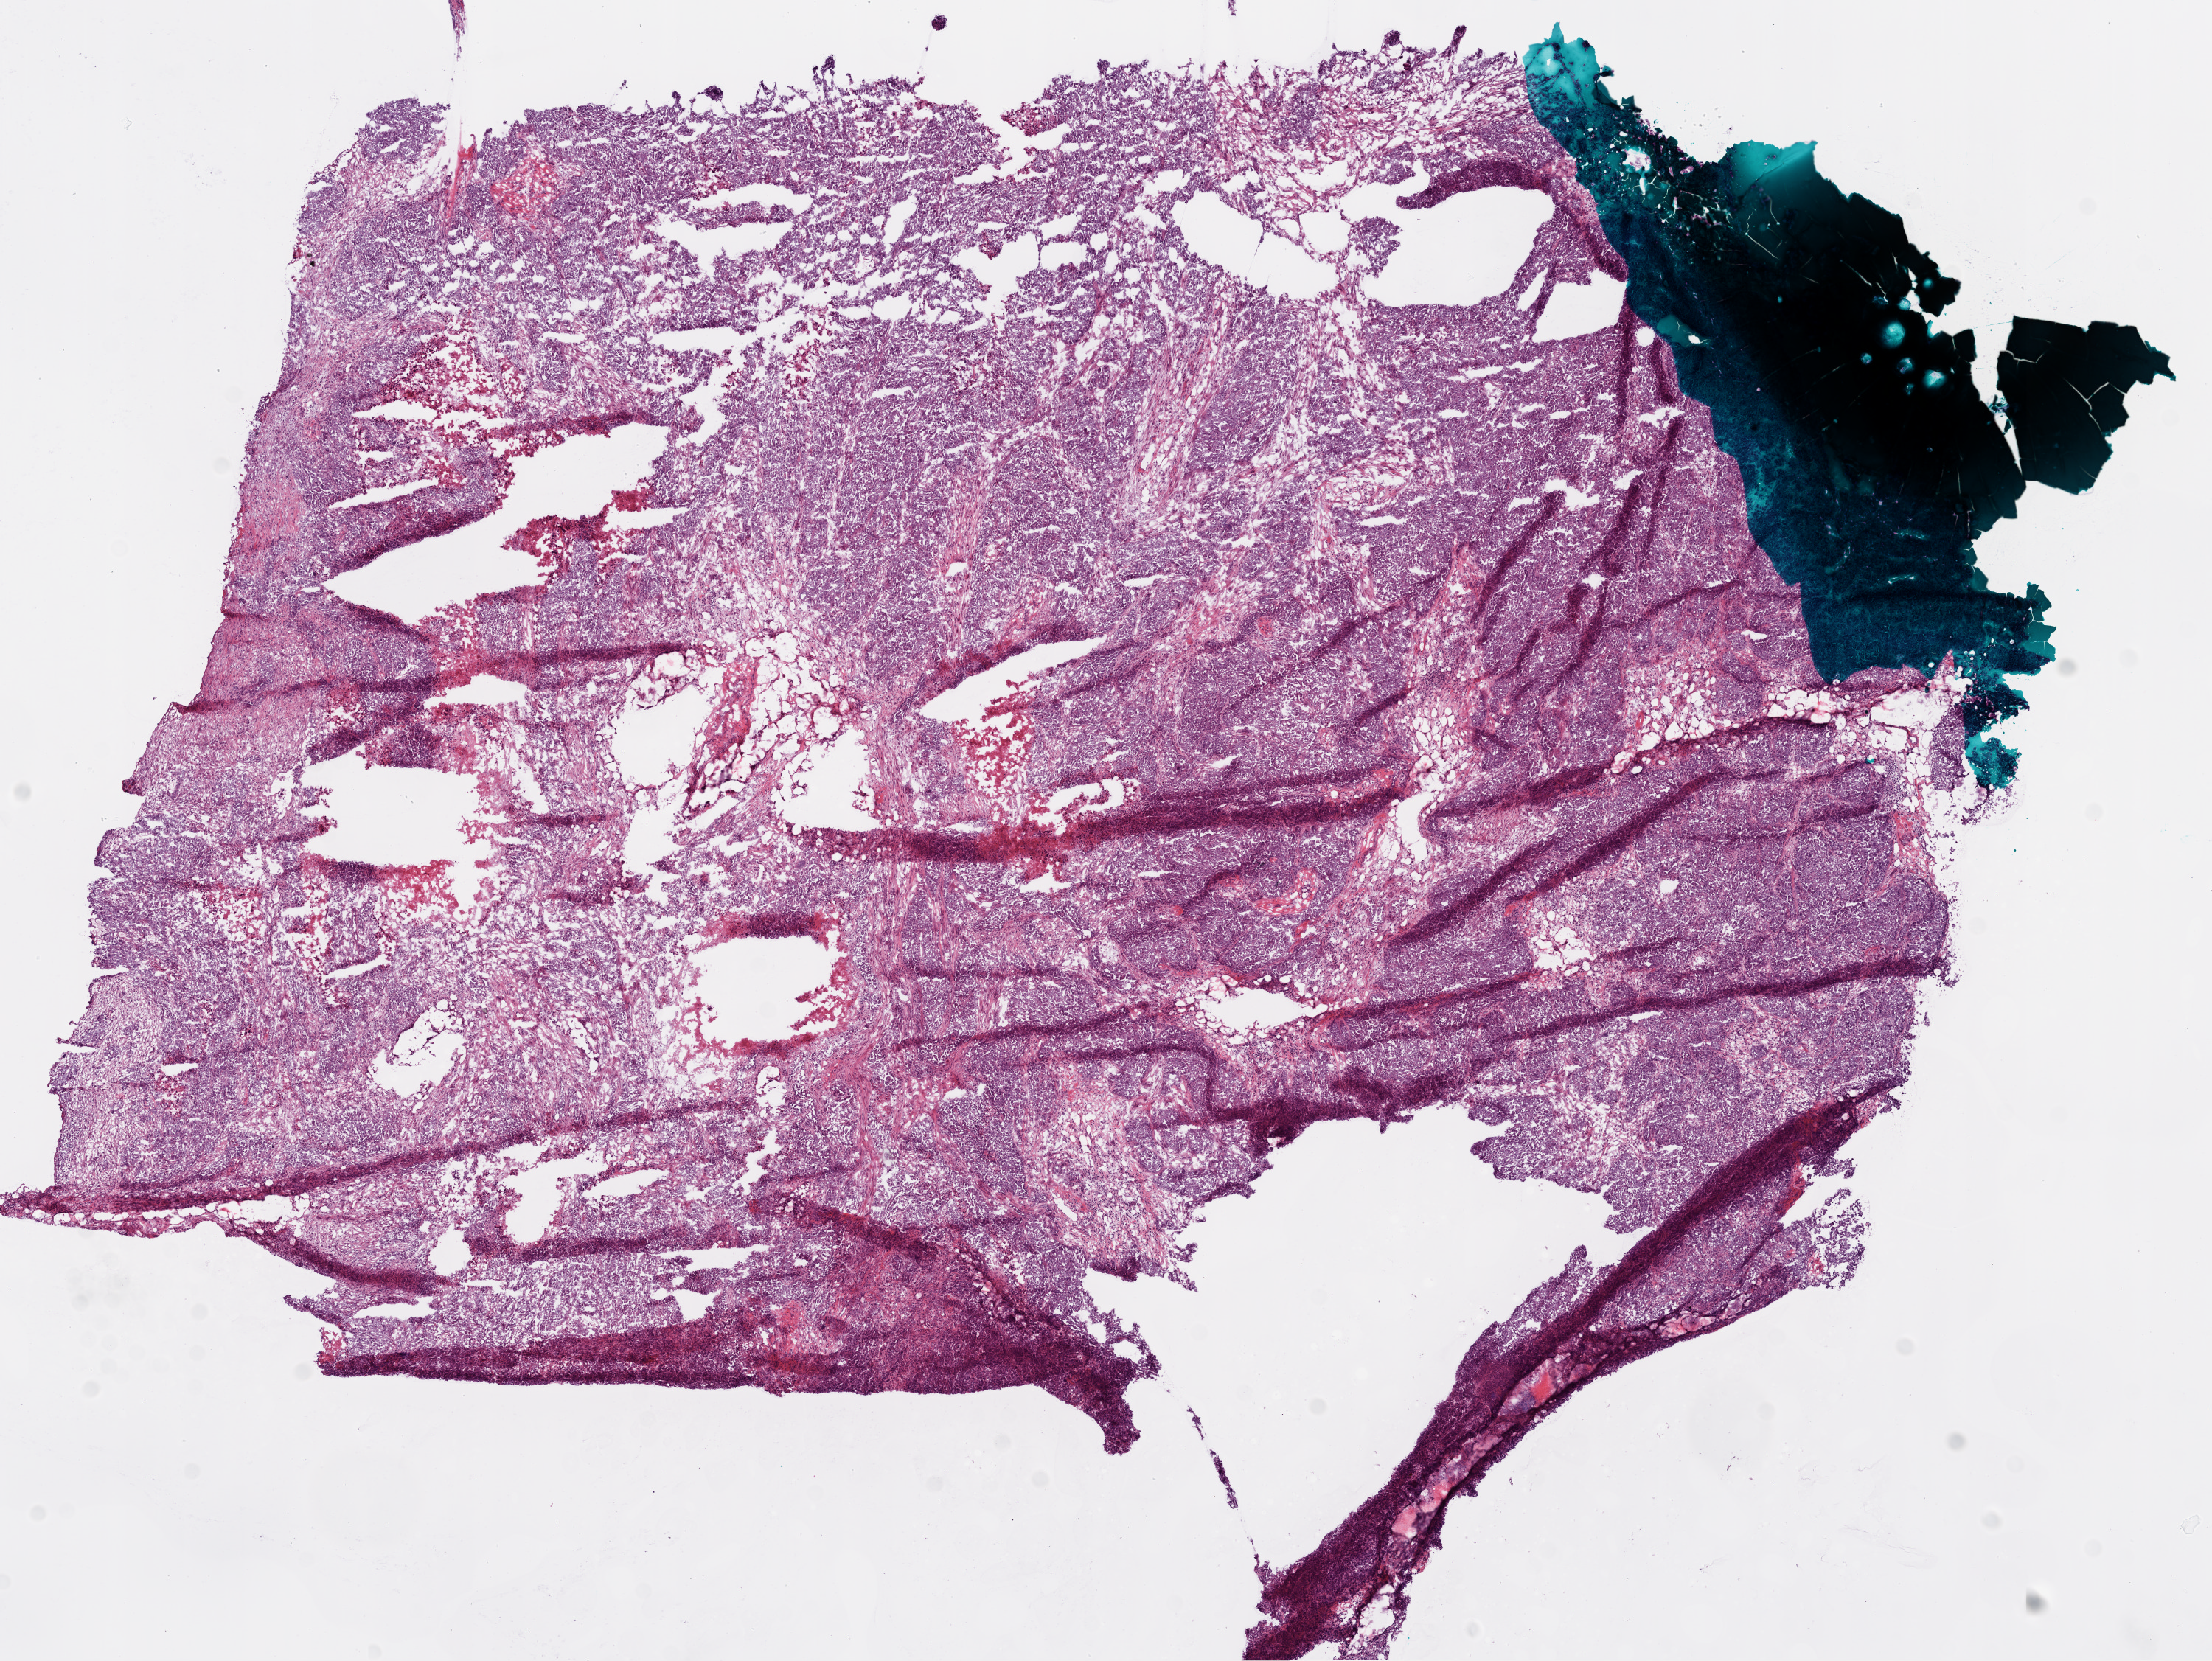
H&E whole-slide image, whole scanned area (about 12.0 x 9.0 mm) shown as a low-resolution overview; frozen section from the bottom of the tissue portion; primary tumour sample from the ovary. Patient: female, age at initial diagnosis 54 years. Histologic grade: G3 (poorly differentiated). Composition of this section per pathologist review: tumour cells 70%, tumour nuclei 85%, normal cells 15%, stromal cells 0%, necrosis 15%.
Laterality: left. Diagnosis: Serous cystadenocarcinoma, NOS. FIGO stage: IV.